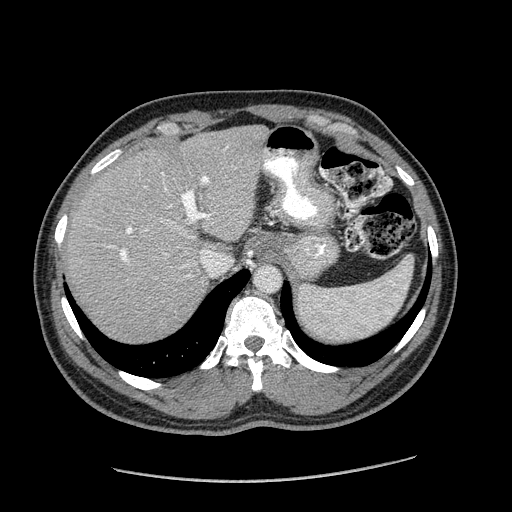
Contrast-enhanced abdominal CT (liver protocol), one axial slice; position 137 of 182 along the scan axis; reconstruction kernel STANDARD; 120 kVp; soft-tissue window (W 400 / L 40 HU); 2.5 mm slice thickness; 512 × 512 image matrix, field of view 400 × 400 mm. Case-level facts recorded for this patient, not image findings: diagnosis: hepatocellular carcinoma (patient treated with transarterial chemoembolisation; whether this scan precedes or follows treatment is not stated here); TNM stage (as recorded): Stage-I; Child-Pugh class: A.
Annotated regions visible in this slice (semi-automatic segmentation, software-assisted and operator-edited):
- liver parenchyma outside the tumour (the mass and vessels are separate outlines, so this box may not span the whole liver): box from (x=66, y=126) to (x=268, y=341) px
- liver vessels: (x=108, y=147)–(x=228, y=277)